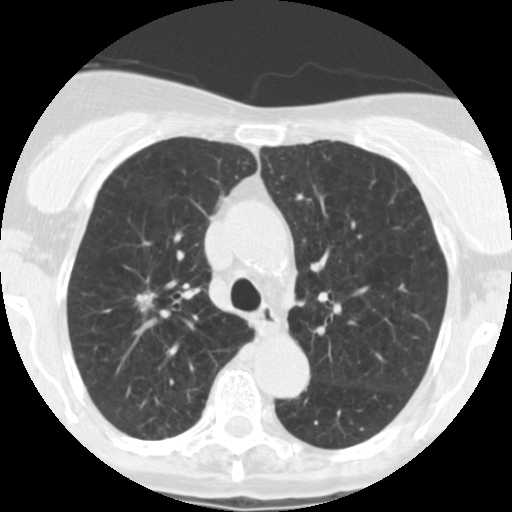
Low-dose screening chest CT, one axial slice. 120 kVp. Lung window (W 1500 / L -600 HU). 2.5 mm slice thickness. 512 × 512 image matrix, field of view 288 × 288 mm.
Annotated regions visible in this slice (manually delineated by an expert):
- lesion 1 (tumor, upper lobe of right lung): bounding box (x1, y1, x2, y2) in pixels: (136, 291, 157, 312)